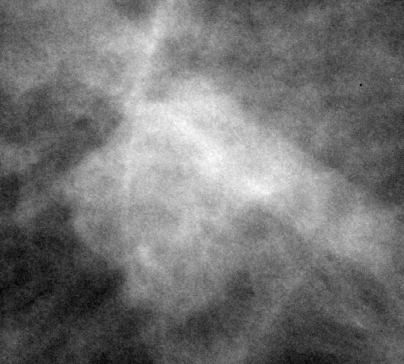
Region of interest cut from a scanned film mammogram (one marked finding); right breast; CC view.
- Marked abnormality: mass, shape oval, margins microlobulated; BI-RADS assessment category 4; pathology (as recorded): benign.